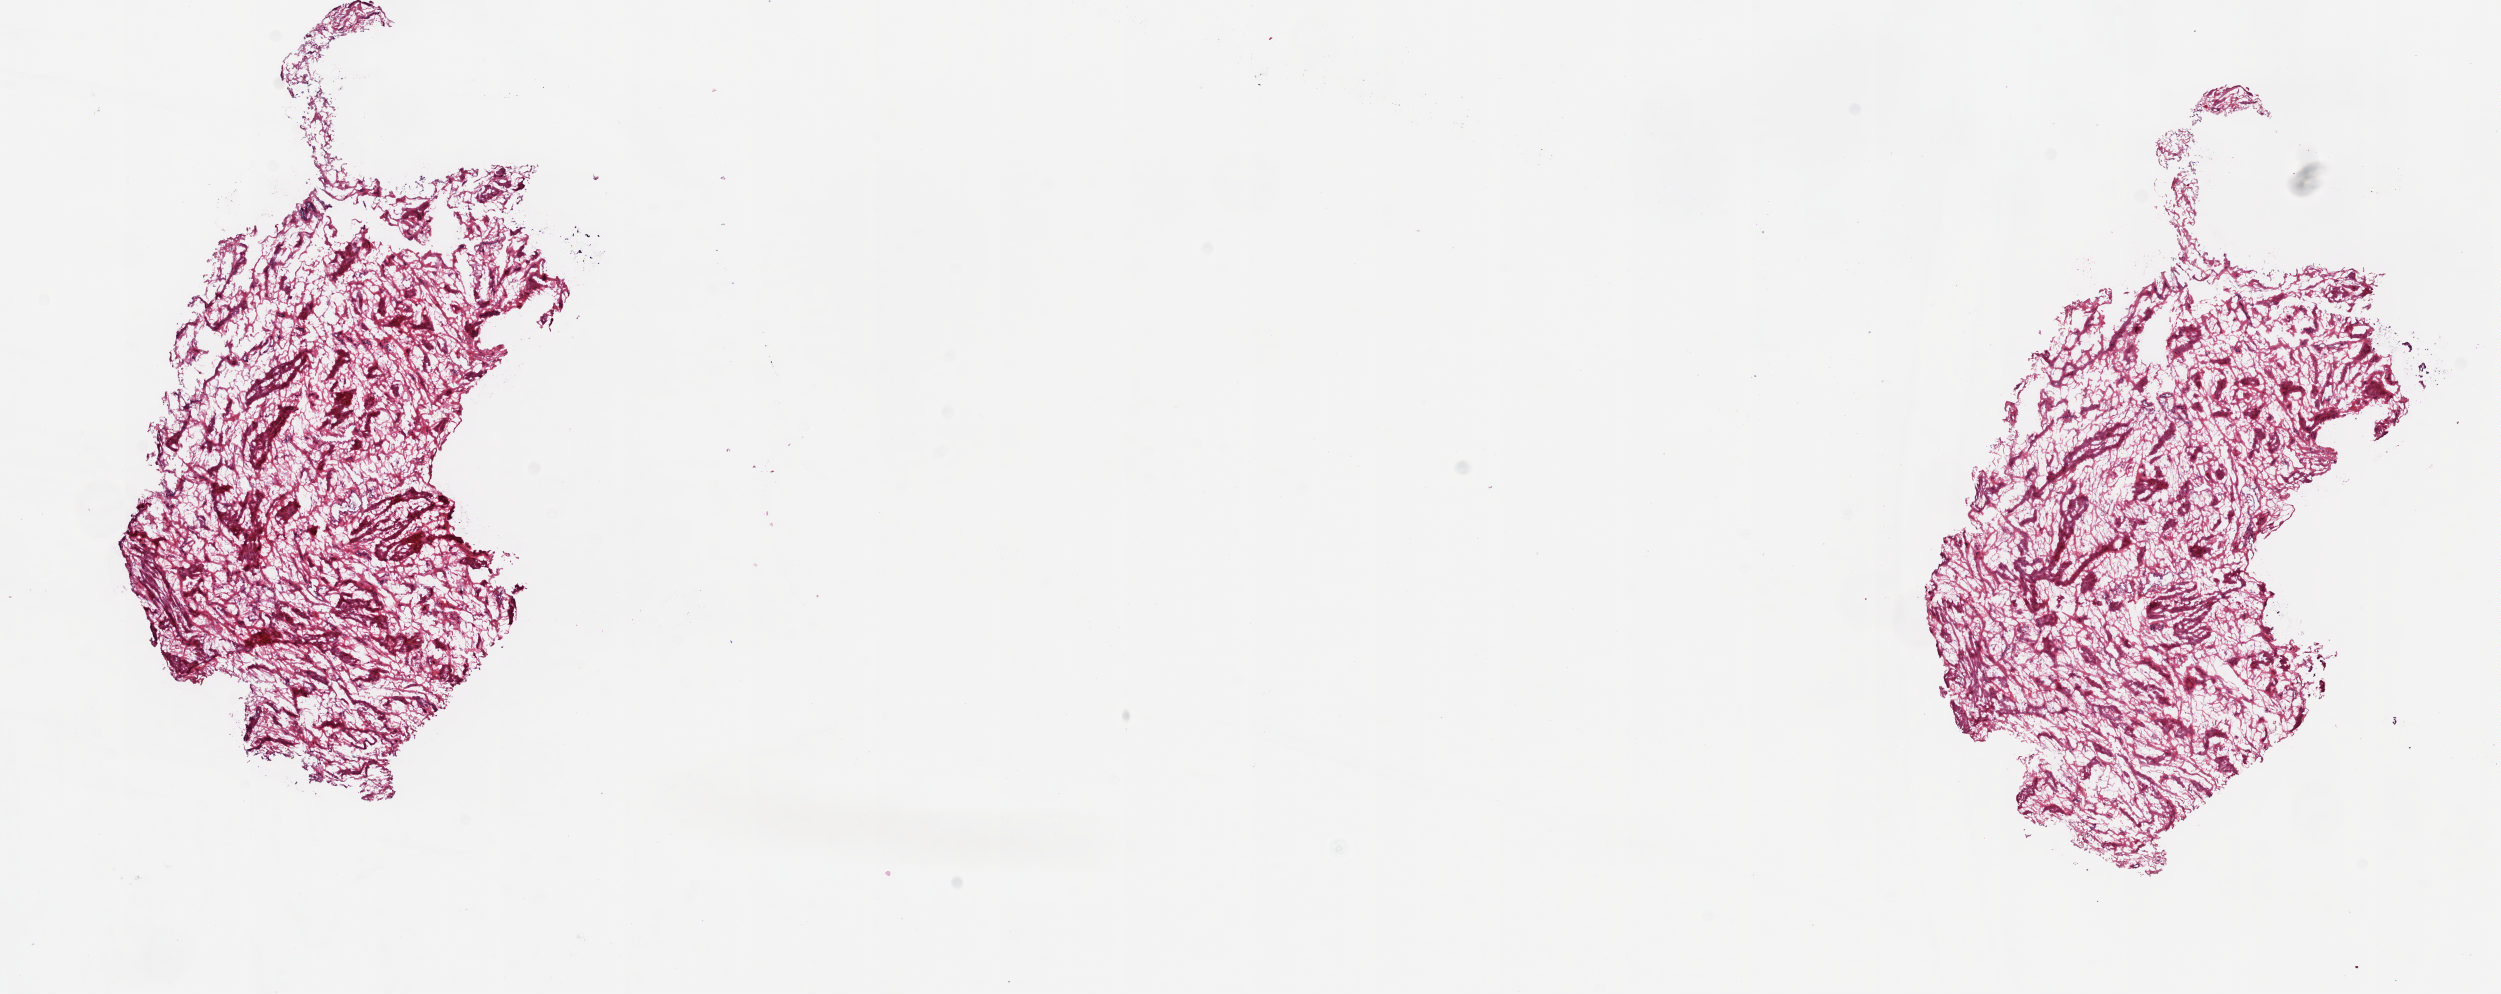
Whole-slide histology image, Hematoxylin and eosin (H&E) stained — low-resolution overview of the scanned area, about 19.8 x 7.9 mm; frozen section from the top of the tissue portion; sample: solid tissue normal (non-tumour tissue), bladder. Female, age 77 years at initial diagnosis. Slide review estimates, as recorded: tumour cells 0%, tumour nuclei 0%, normal cells 0%, stromal cells 100%, necrosis 0%. Inflammatory infiltration, as recorded: lymphocyte infiltration 1%, monocyte infiltration 0%, neutrophil infiltration 0%.
This section: solid tissue normal sample (biorepository sample class). Patient diagnosis: Transitional cell carcinoma.